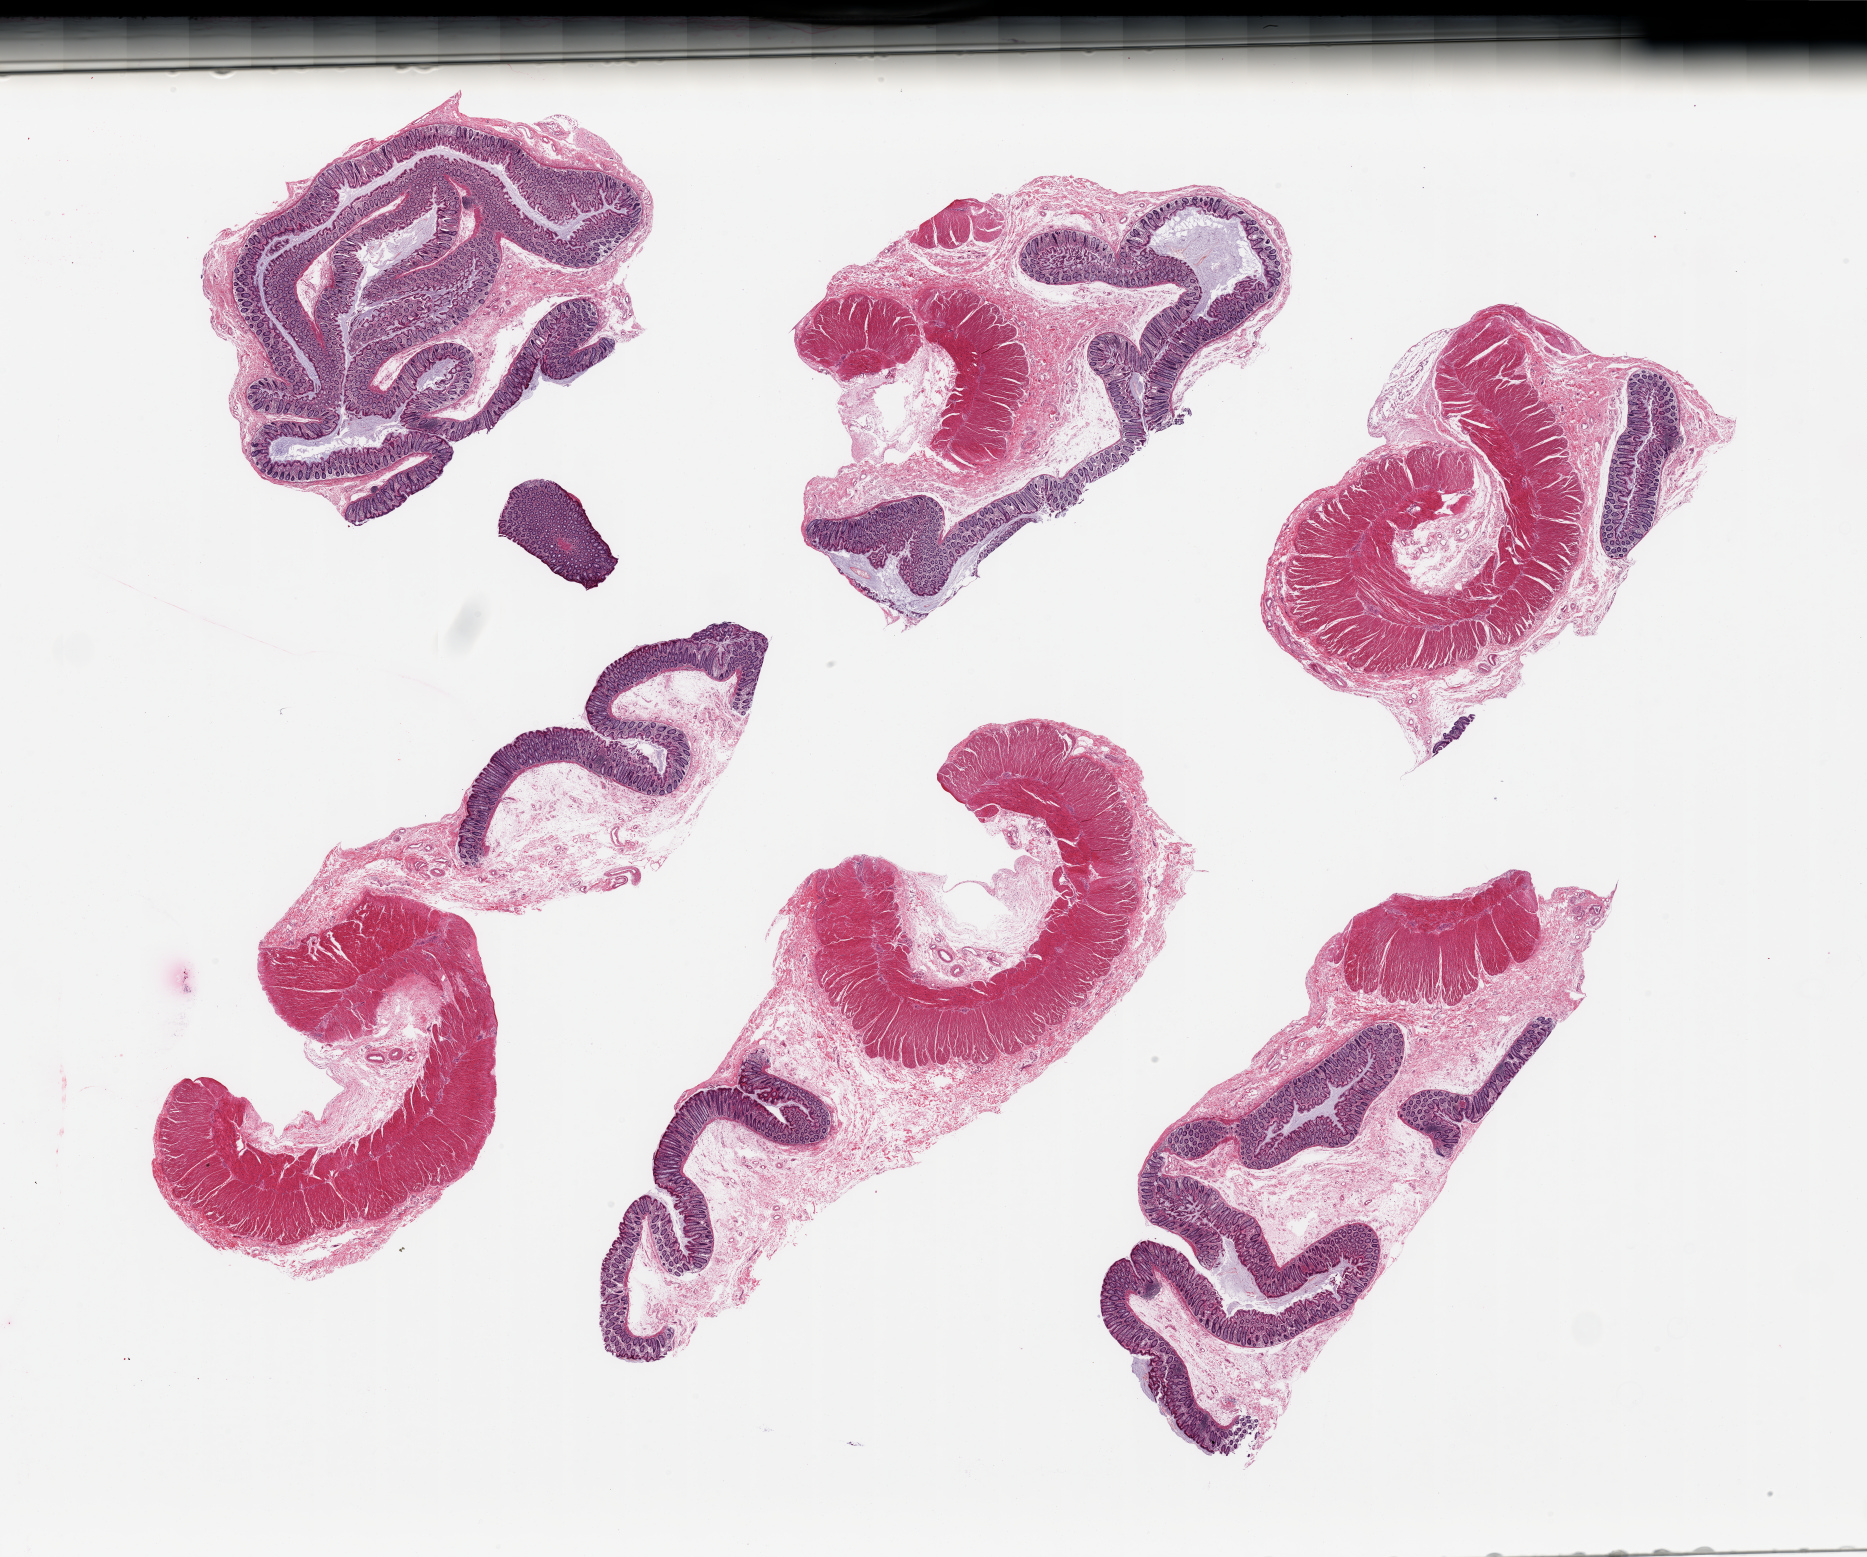
Digitized H&E-stained section, low-resolution overview of the scanned area, about 29.5 x 24.6 mm. PAXgene-fixed paraffin-embedded (PFPE) section. Section of transverse colon (target tissue). Donor tissue sample. Female donor.
- pathologist's review note for this sample: 6 pieces, fragmented, target mucosa well-fixed, up to ~0.5mm